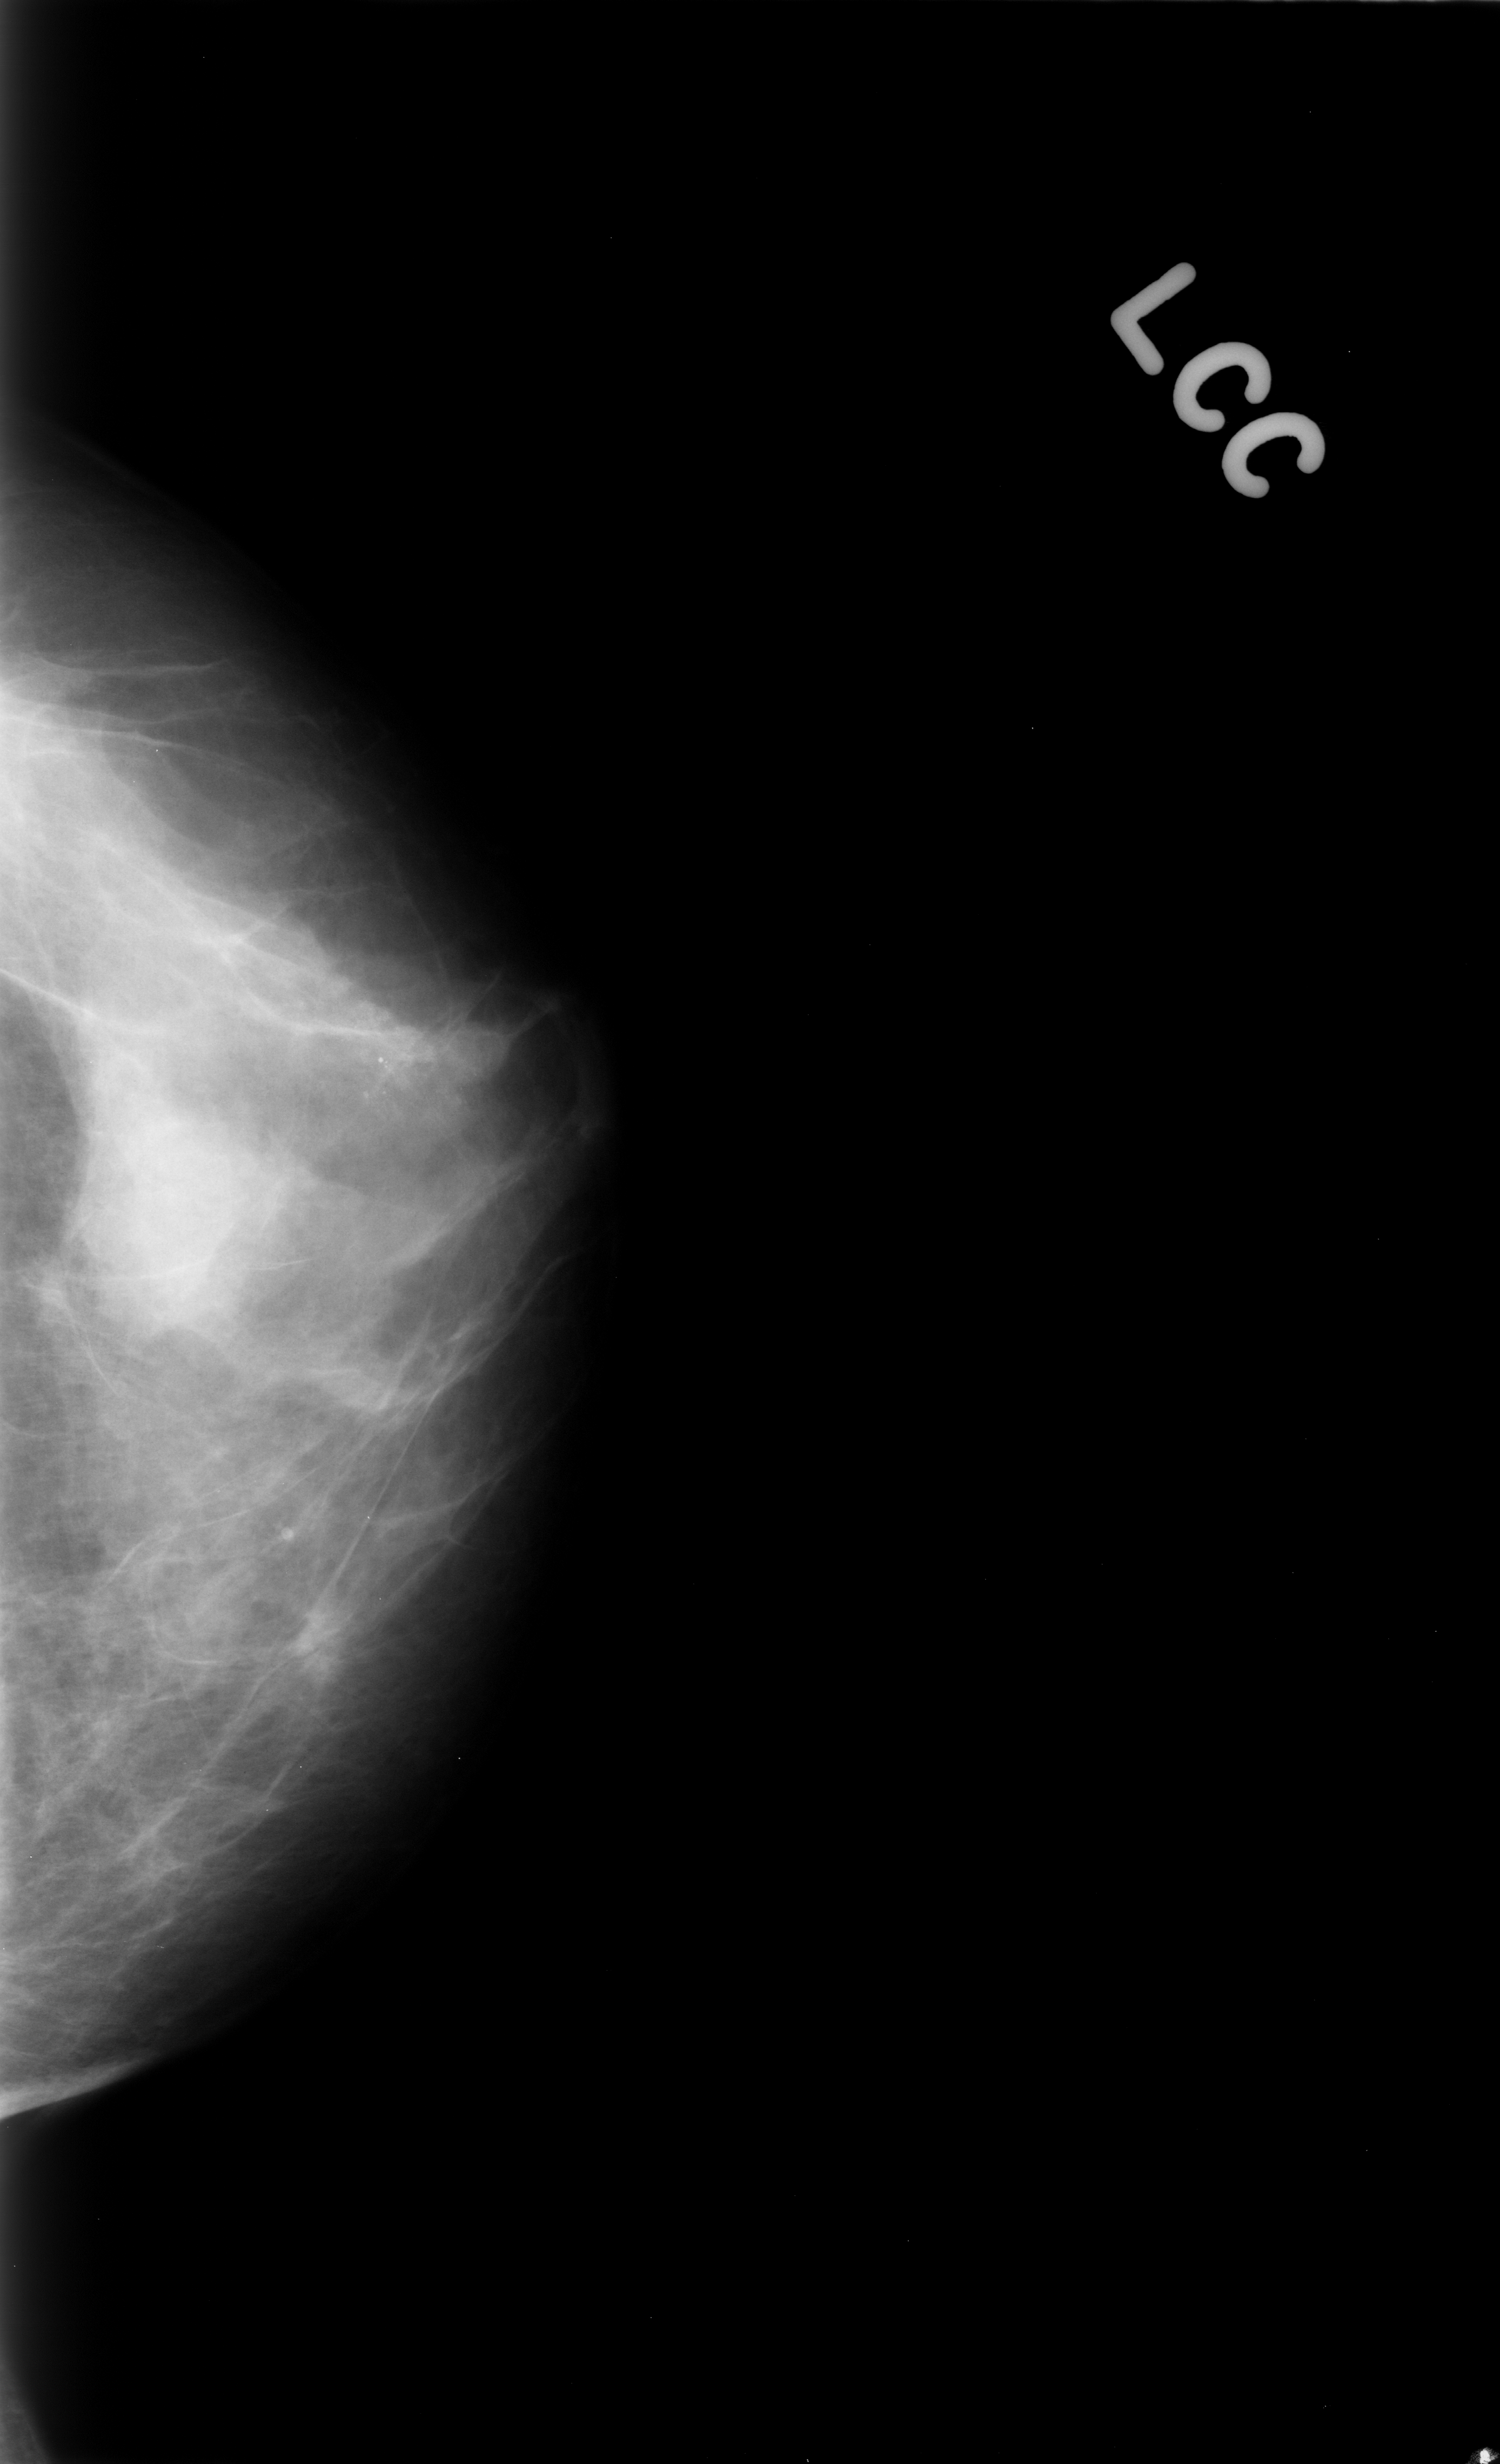
Scanned film-screen mammogram, left breast, craniocaudal (CC) view, breast composition: heterogeneously dense (BI-RADS density category 3 of 4).
Marked findings (only marked abnormalities are described; nothing is implied about the rest of the image): calcifications, morphology pleomorphic, distribution clustered; BI-RADS assessment category 4; pathology result (as recorded, not read from the image): benign.